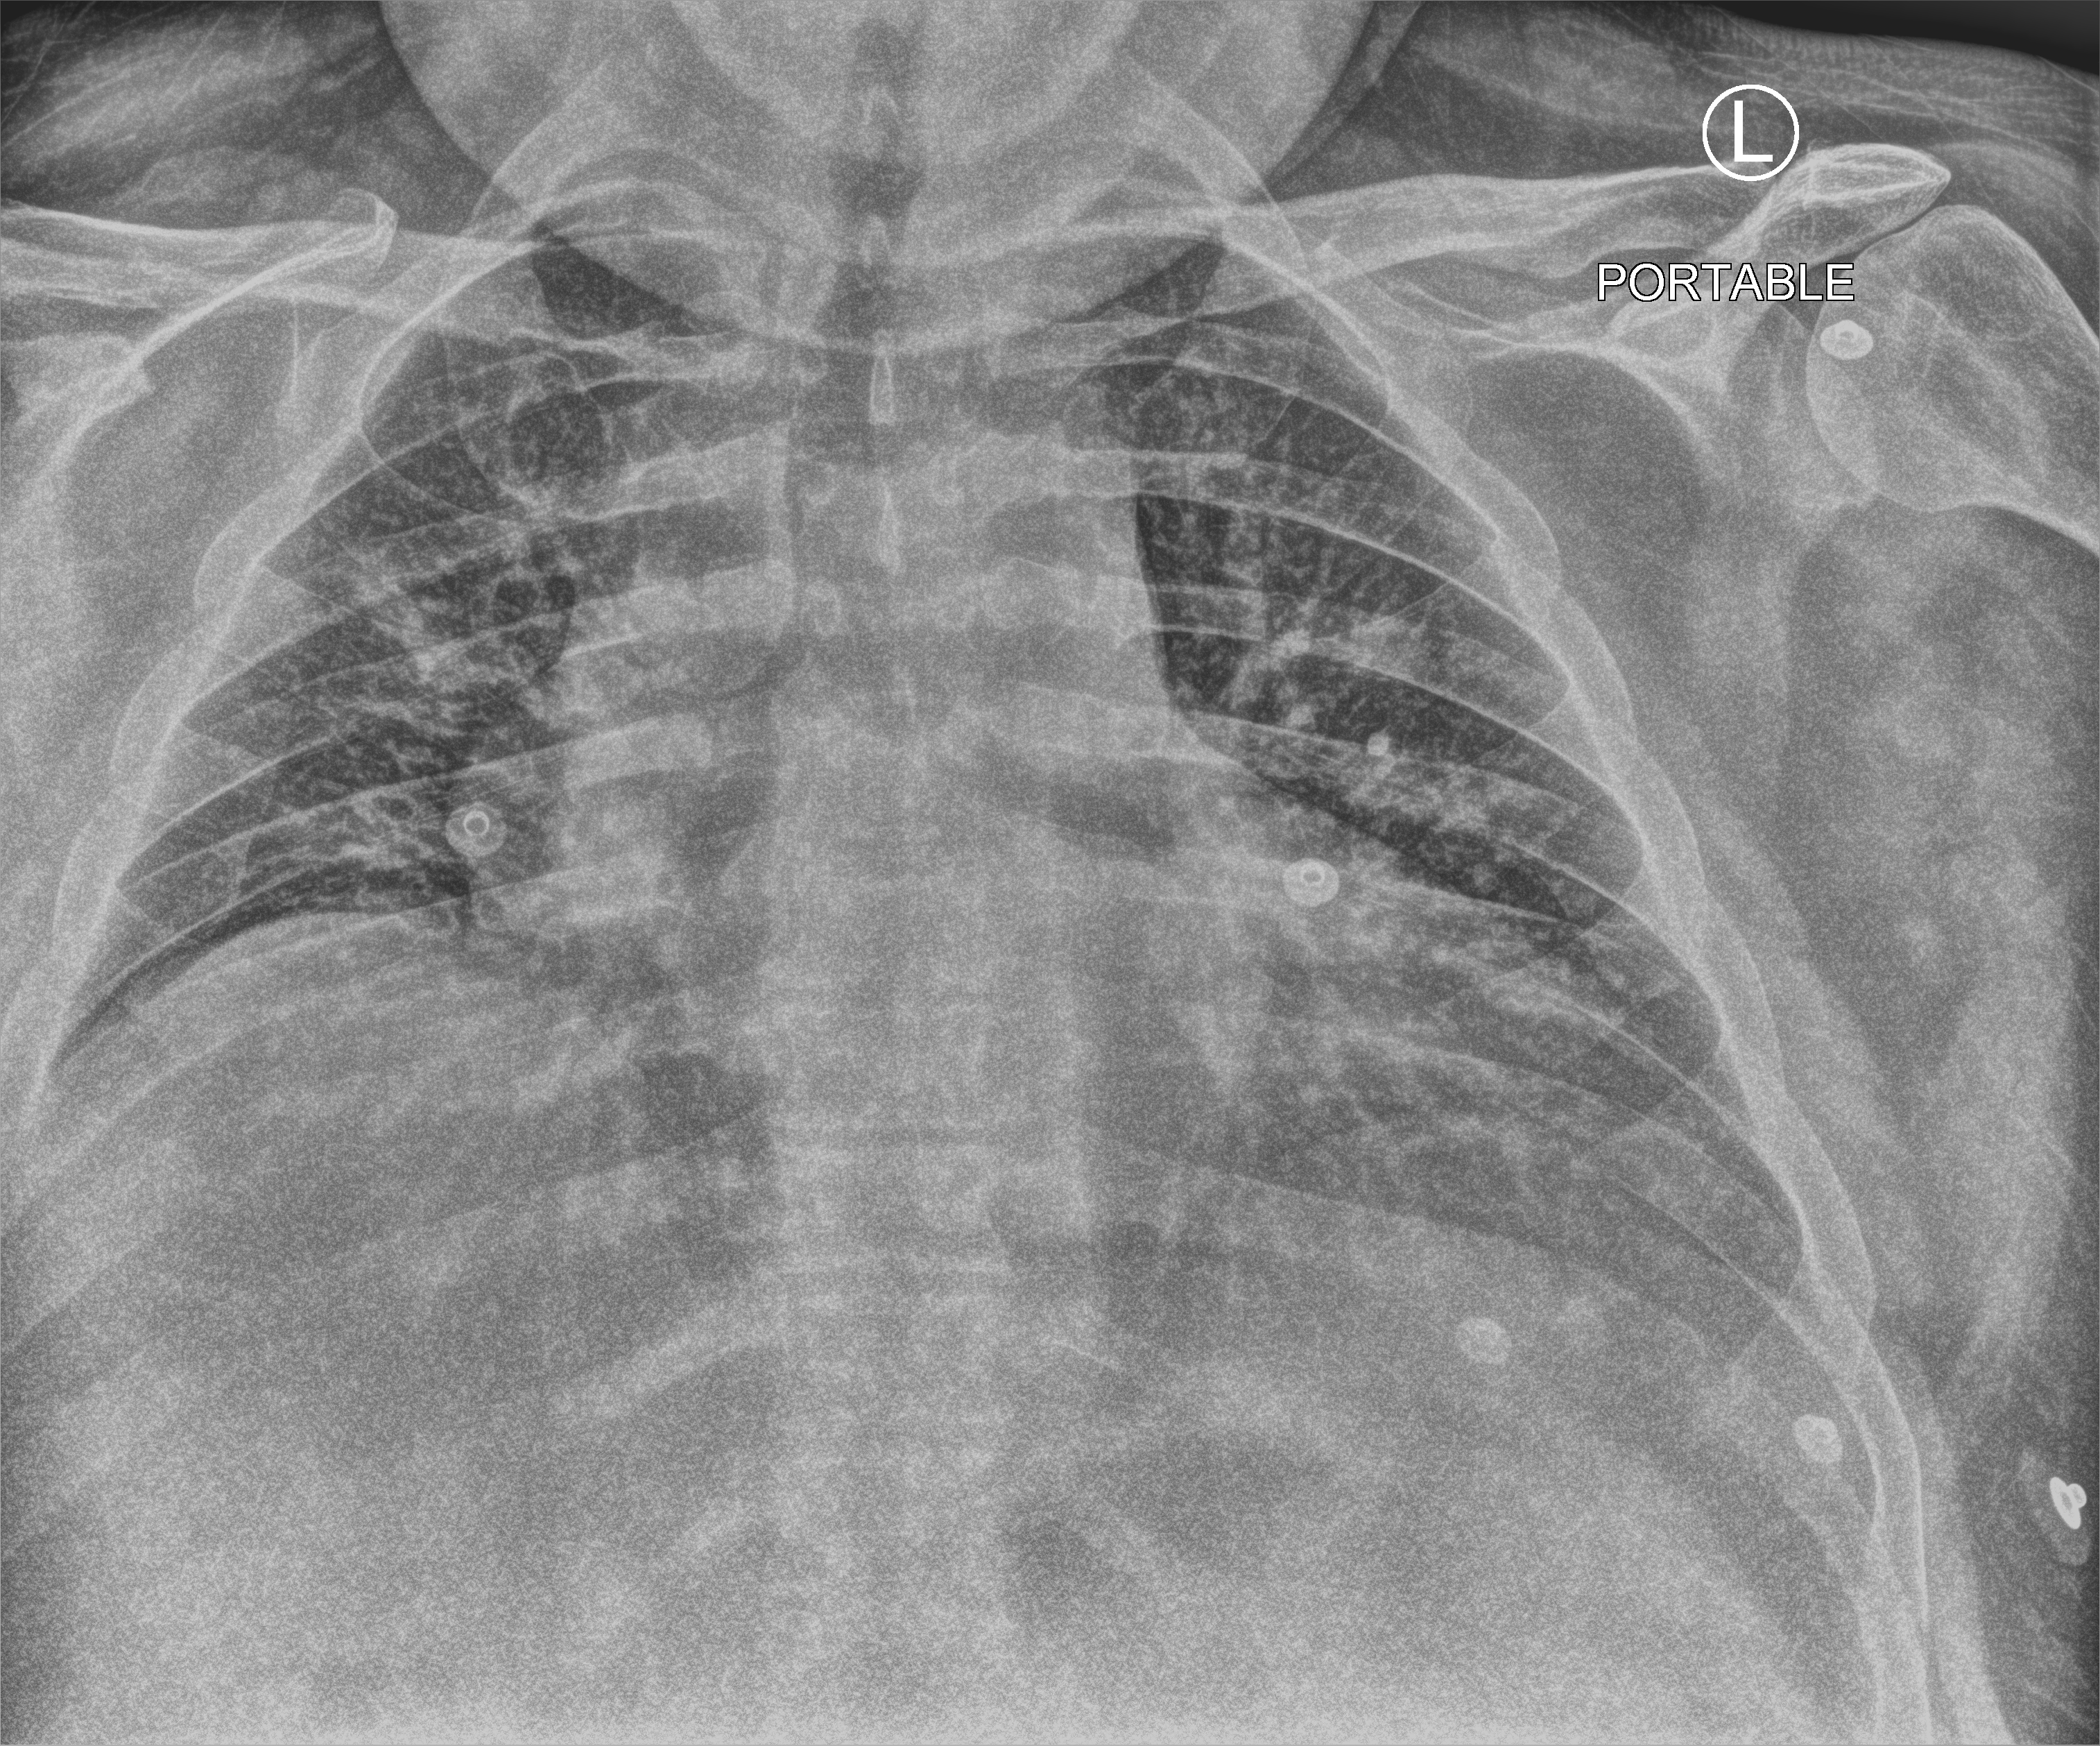
Portable chest radiograph, anteroposterior (AP) projection. Male patient hospitalised with COVID-19, age 18–59 years.
Admission-level facts for this patient (not findings on this image; timing relative to this image not recorded): admitted to intensive care during this hospital stay: no.